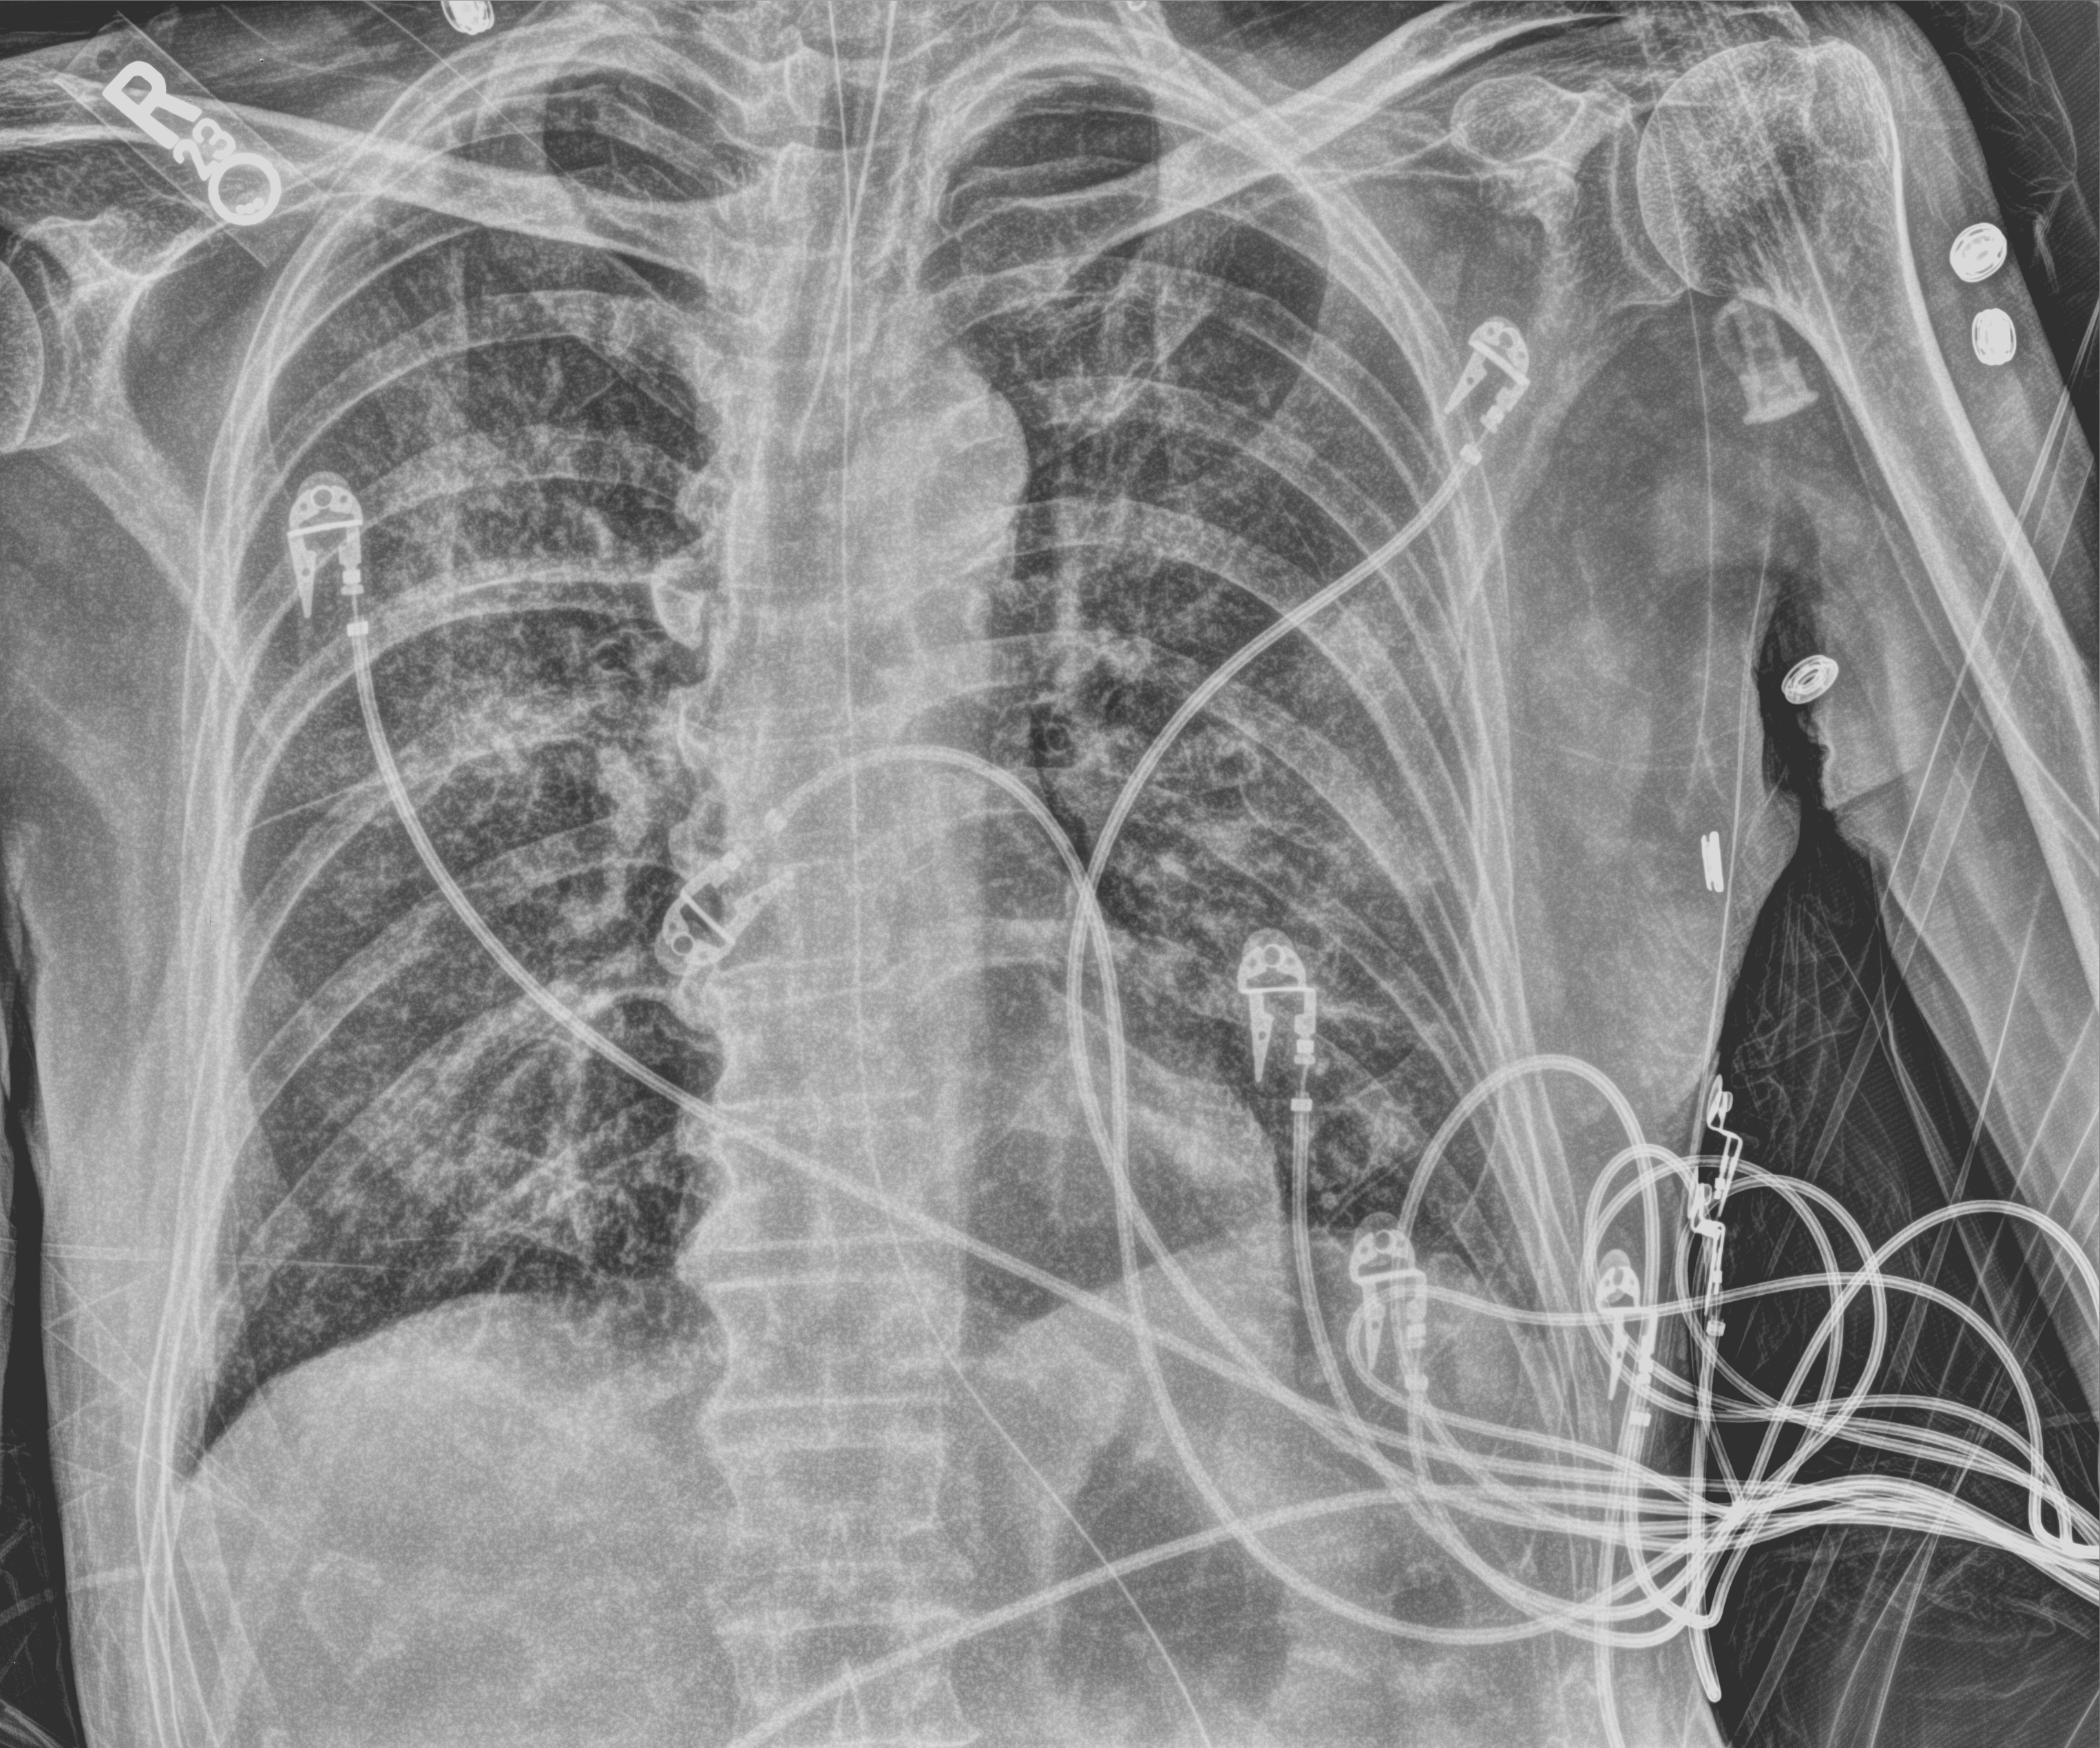
Portable chest radiograph, anteroposterior (AP) projection. Patient hospitalised with COVID-19; male, aged 60–74 years.
Hospital-stay facts (about this admission, not read from this image; timing relative to this image not recorded):
- mechanically ventilated during this hospital stay: yes
- smoking status (admission record): current